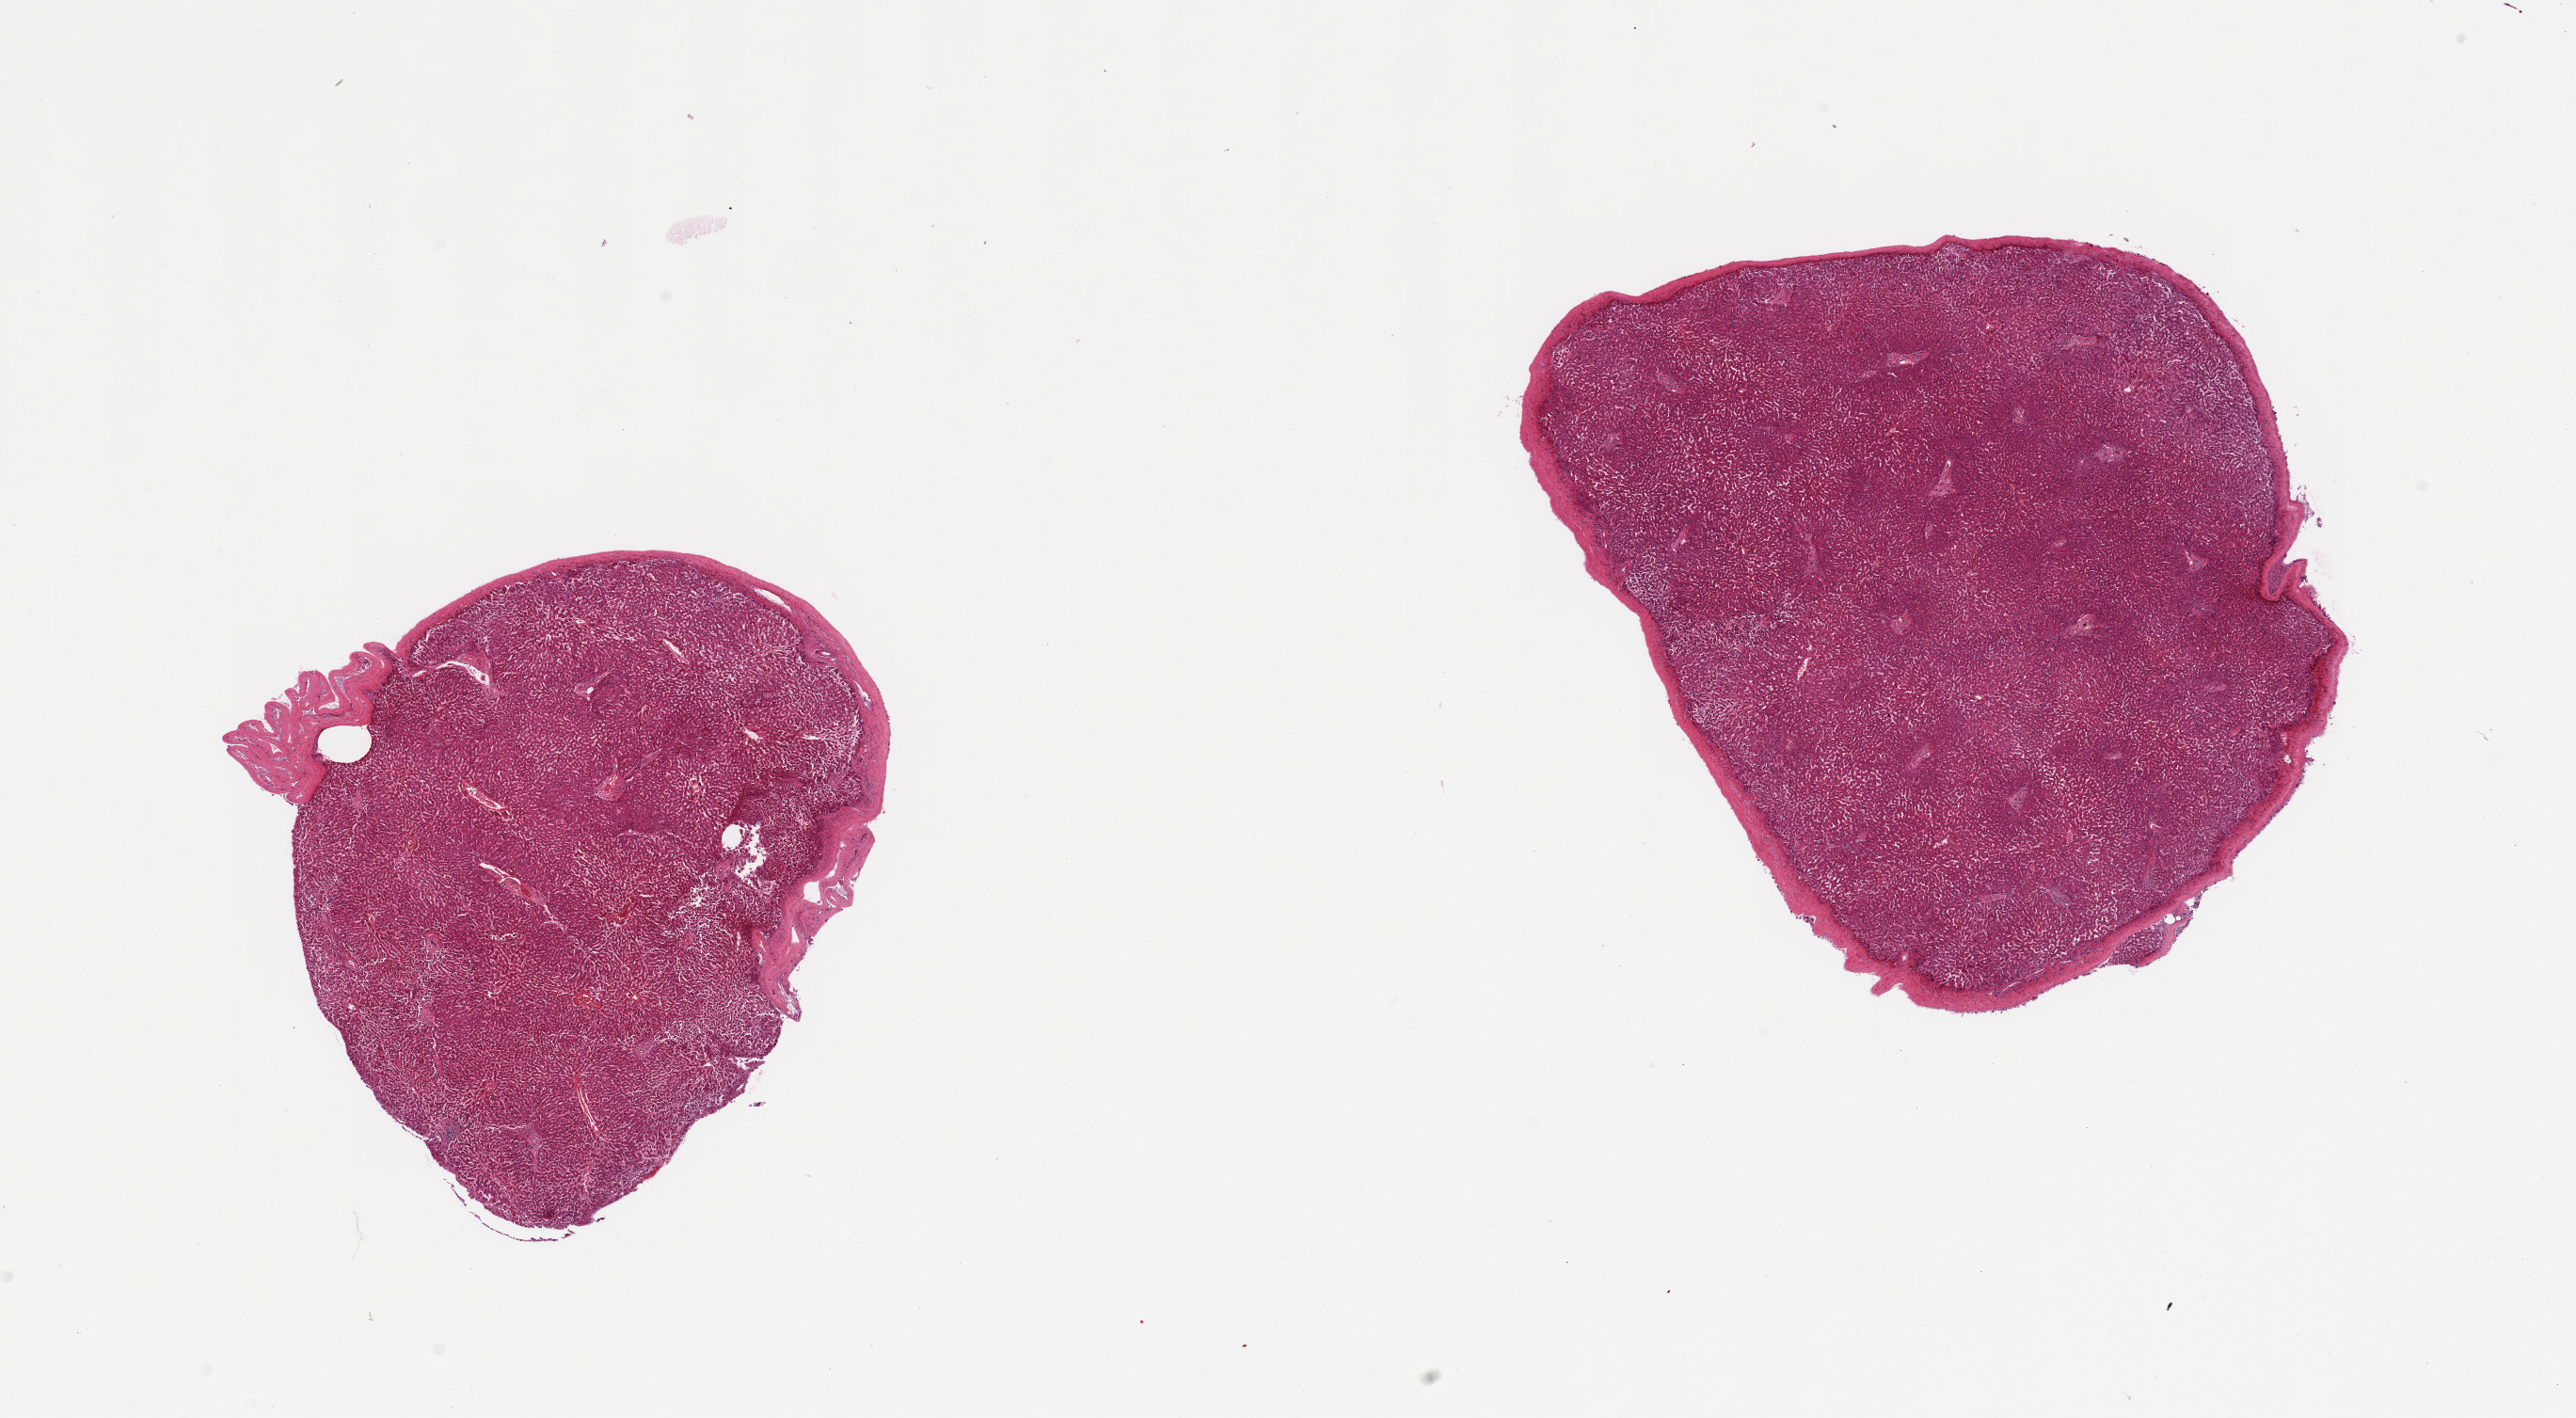
Digitized hematoxylin and eosin (H&E)-stained section, whole scanned area (about 21.7 x 11.9 mm) shown as a low-resolution overview; PAXgene-fixed, paraffin-embedded tissue; section of liver (target tissue); donor tissue sample.
Review note (as recorded): 2 pieces; capsule included.